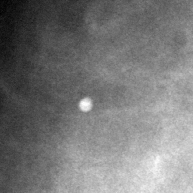
Region of interest cut from a scanned film mammogram (one marked finding); right breast; CC view; BI-RADS breast density category 3 (scale 1–4).
Finding: calcifications, morphology punctate; BI-RADS assessment category 2; subtlety rating 3 on a 1 (subtle) to 5 (obvious) scale; benign without callback (not worked up further).